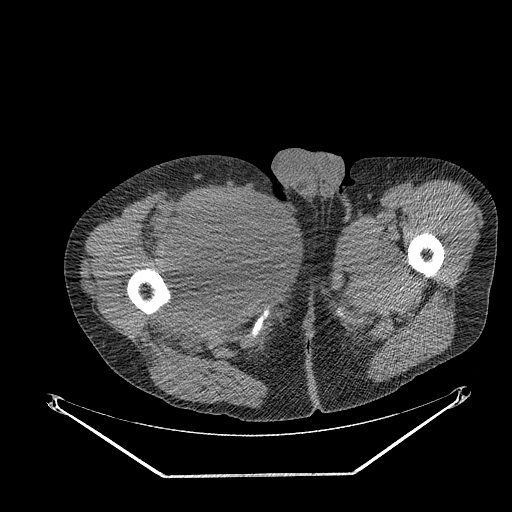
CT of an extremity soft-tissue mass (from a PET/CT study), one axial slice. Slice 281 of 311 in the series (ordered by position). Reconstruction kernel STANDARD. 140 kVp. Soft-tissue window (W 400 / L 40 HU). 3.75 mm slice thickness. 512 × 512 image matrix, field of view 500 × 500 mm. Male patient. Case-level facts recorded for this patient, not image findings: histological type: undifferentiated - pleiomorphic; grade: high; site of the primary tumour: right thigh.
Annotated regions visible in this slice (expert contour drawn on MRI and transferred to this co-registered scan by the dataset authors):
- gross tumour volume including surrounding oedema: bounding box [x1, y1, x2, y2] px = [178, 192, 261, 277]
- gross tumour volume (mass): [178, 196, 259, 275]